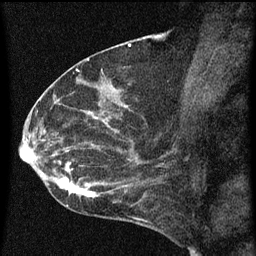
Breast MRI (dynamic contrast-enhanced), one sagittal slice; slice 36 of 60 in the series (ordered by position); dynamic contrast-enhanced series, image 2 of 3 at this slice position (ordered by acquisition); 1.5 T; TE 4.2 ms, TR 8 ms; 2 mm slice thickness; 256 × 256 image matrix, field of view 180 × 180 mm. Female patient, age 54 years.
Outlined on this slice (semi-automatically segmented with operator editing):
- analysis volume of interest (the breast-tissue region the enhancement analysis was run in; not a lesion): bounding box <49,138,164,209> (left, top, right, bottom; pixels)
- tumour enhancement mask (voxels above the 70 % enhancement threshold inside the analysis volume of interest): <50,140,157,207>